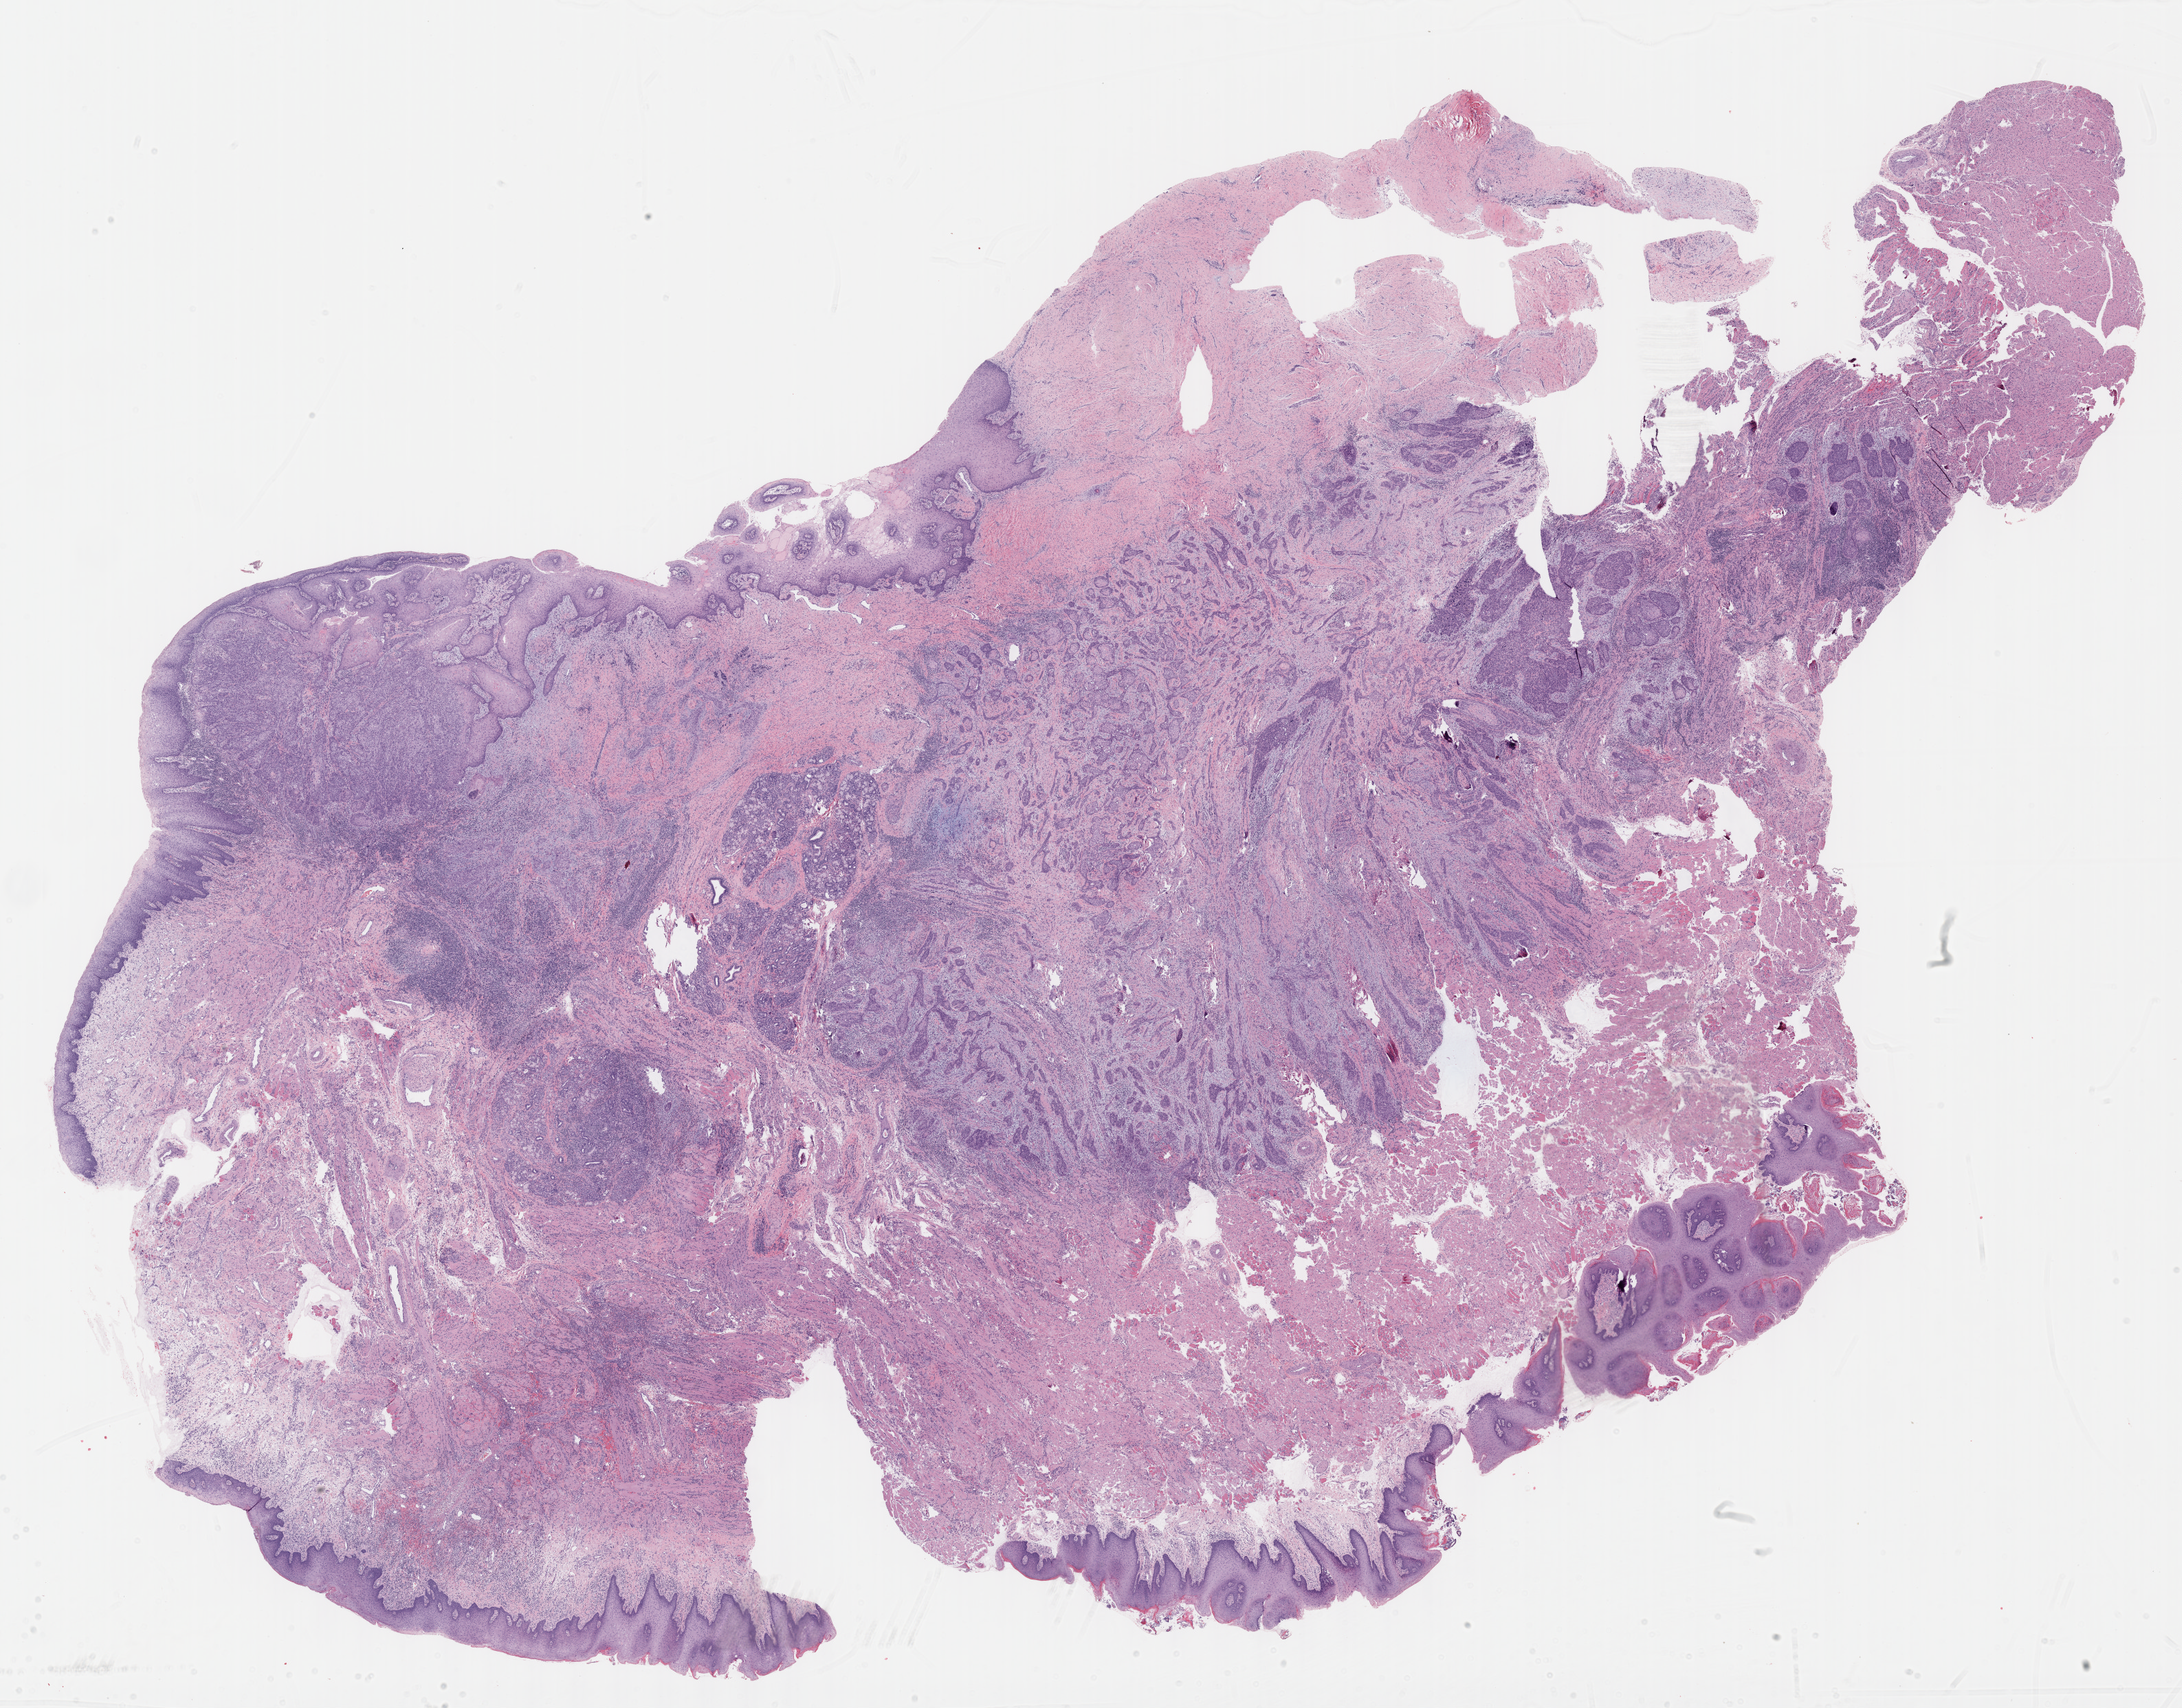
Whole-slide histology image, H&E — whole scanned area (about 25.7 x 20.1 mm, from a 40x scan) shown as a low-resolution overview; formalin-fixed paraffin-embedded (FFPE) diagnostic section; primary tumour sample from the head and neck. Female patient; age at initial diagnosis 61 years.
Pathologic diagnosis: Squamous cell carcinoma, NOS.